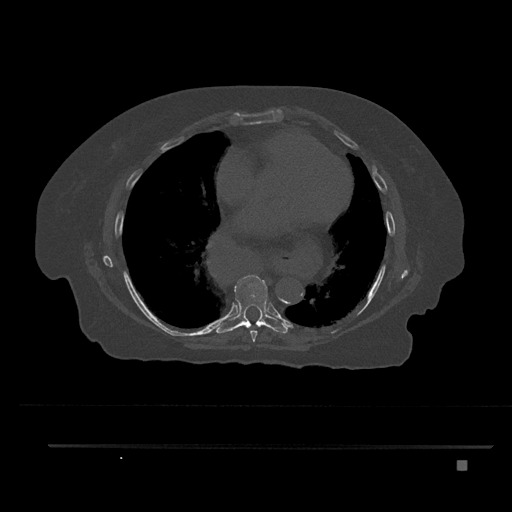
CT including the spine, one axial slice. Position 455 of 797 along the scan axis. 120 kVp. Bone window (W 1800 / L 400 HU). 0.5 mm slice thickness. 512 × 512 image matrix. Female patient, age 76 years. Case-level facts recorded for this patient, not image findings: primary cancer: lung.
Annotated regions visible in this slice (semi-automatic segmentation, software-assisted and operator-edited):
- T7 vertebra: bounding box (x1, y1, x2, y2) in pixels: (250, 329, 257, 342)
- T8 vertebra: (216, 275, 288, 334)